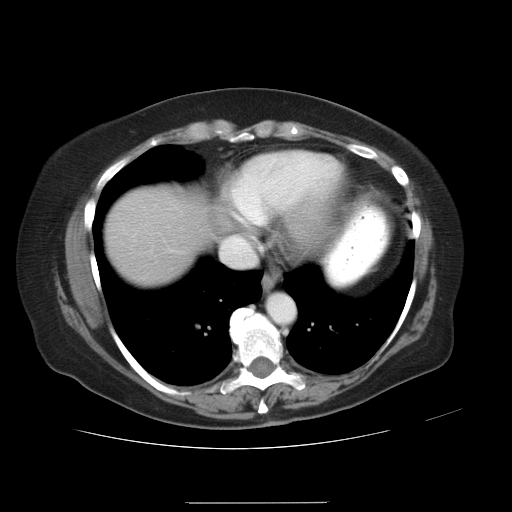
Contrast-enhanced abdominal CT, one axial slice; position 28 of 32 along the scan axis; reconstruction kernel STANDARD; intravenous contrast given; soft-tissue window (W 400 / L 40 HU); 7.5 mm slice thickness; 512 × 512 image matrix, field of view 386 × 386 mm. Female patient, age 65 years. From the clinical record (not read from this slice): diagnosis: colorectal cancer liver metastases, imaged before liver resection; multiple liver metastases: yes; largest metastasis: 1.7 cm; disease in both lobes: no.
Structures marked on this image (manually delineated by an expert):
- liver: bounding box <106,189,210,283> (left, top, right, bottom; pixels)
- planned liver remnant (the part of the liver to remain after resection): <107,189,210,283>